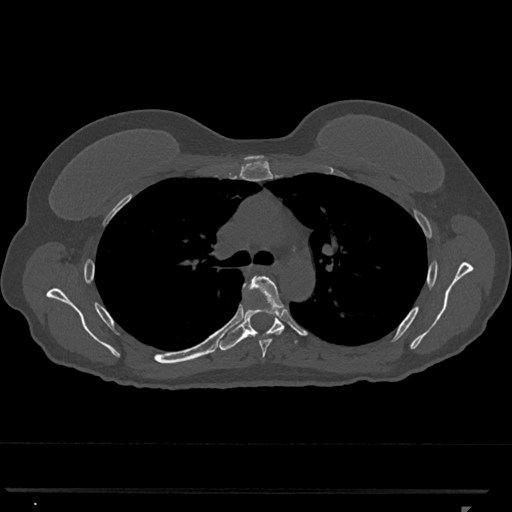
CT including the spine, one axial slice. Slice 784 of 793 in the series (ordered by position). Reconstruction kernel Br40s/3. 120 kVp. Bone window (W 1800 / L 400 HU). 0.5 mm slice thickness. 512 × 512 image matrix. Patient: female, 62 years. From the clinical record (not read from this slice): primary cancer: renal.
Outlined on this slice (semi-automatic segmentation, software-assisted and operator-edited):
- T5 vertebra: box from (x=249, y=275) to (x=284, y=358) px
- T6 vertebra: (x=219, y=281)–(x=298, y=351)